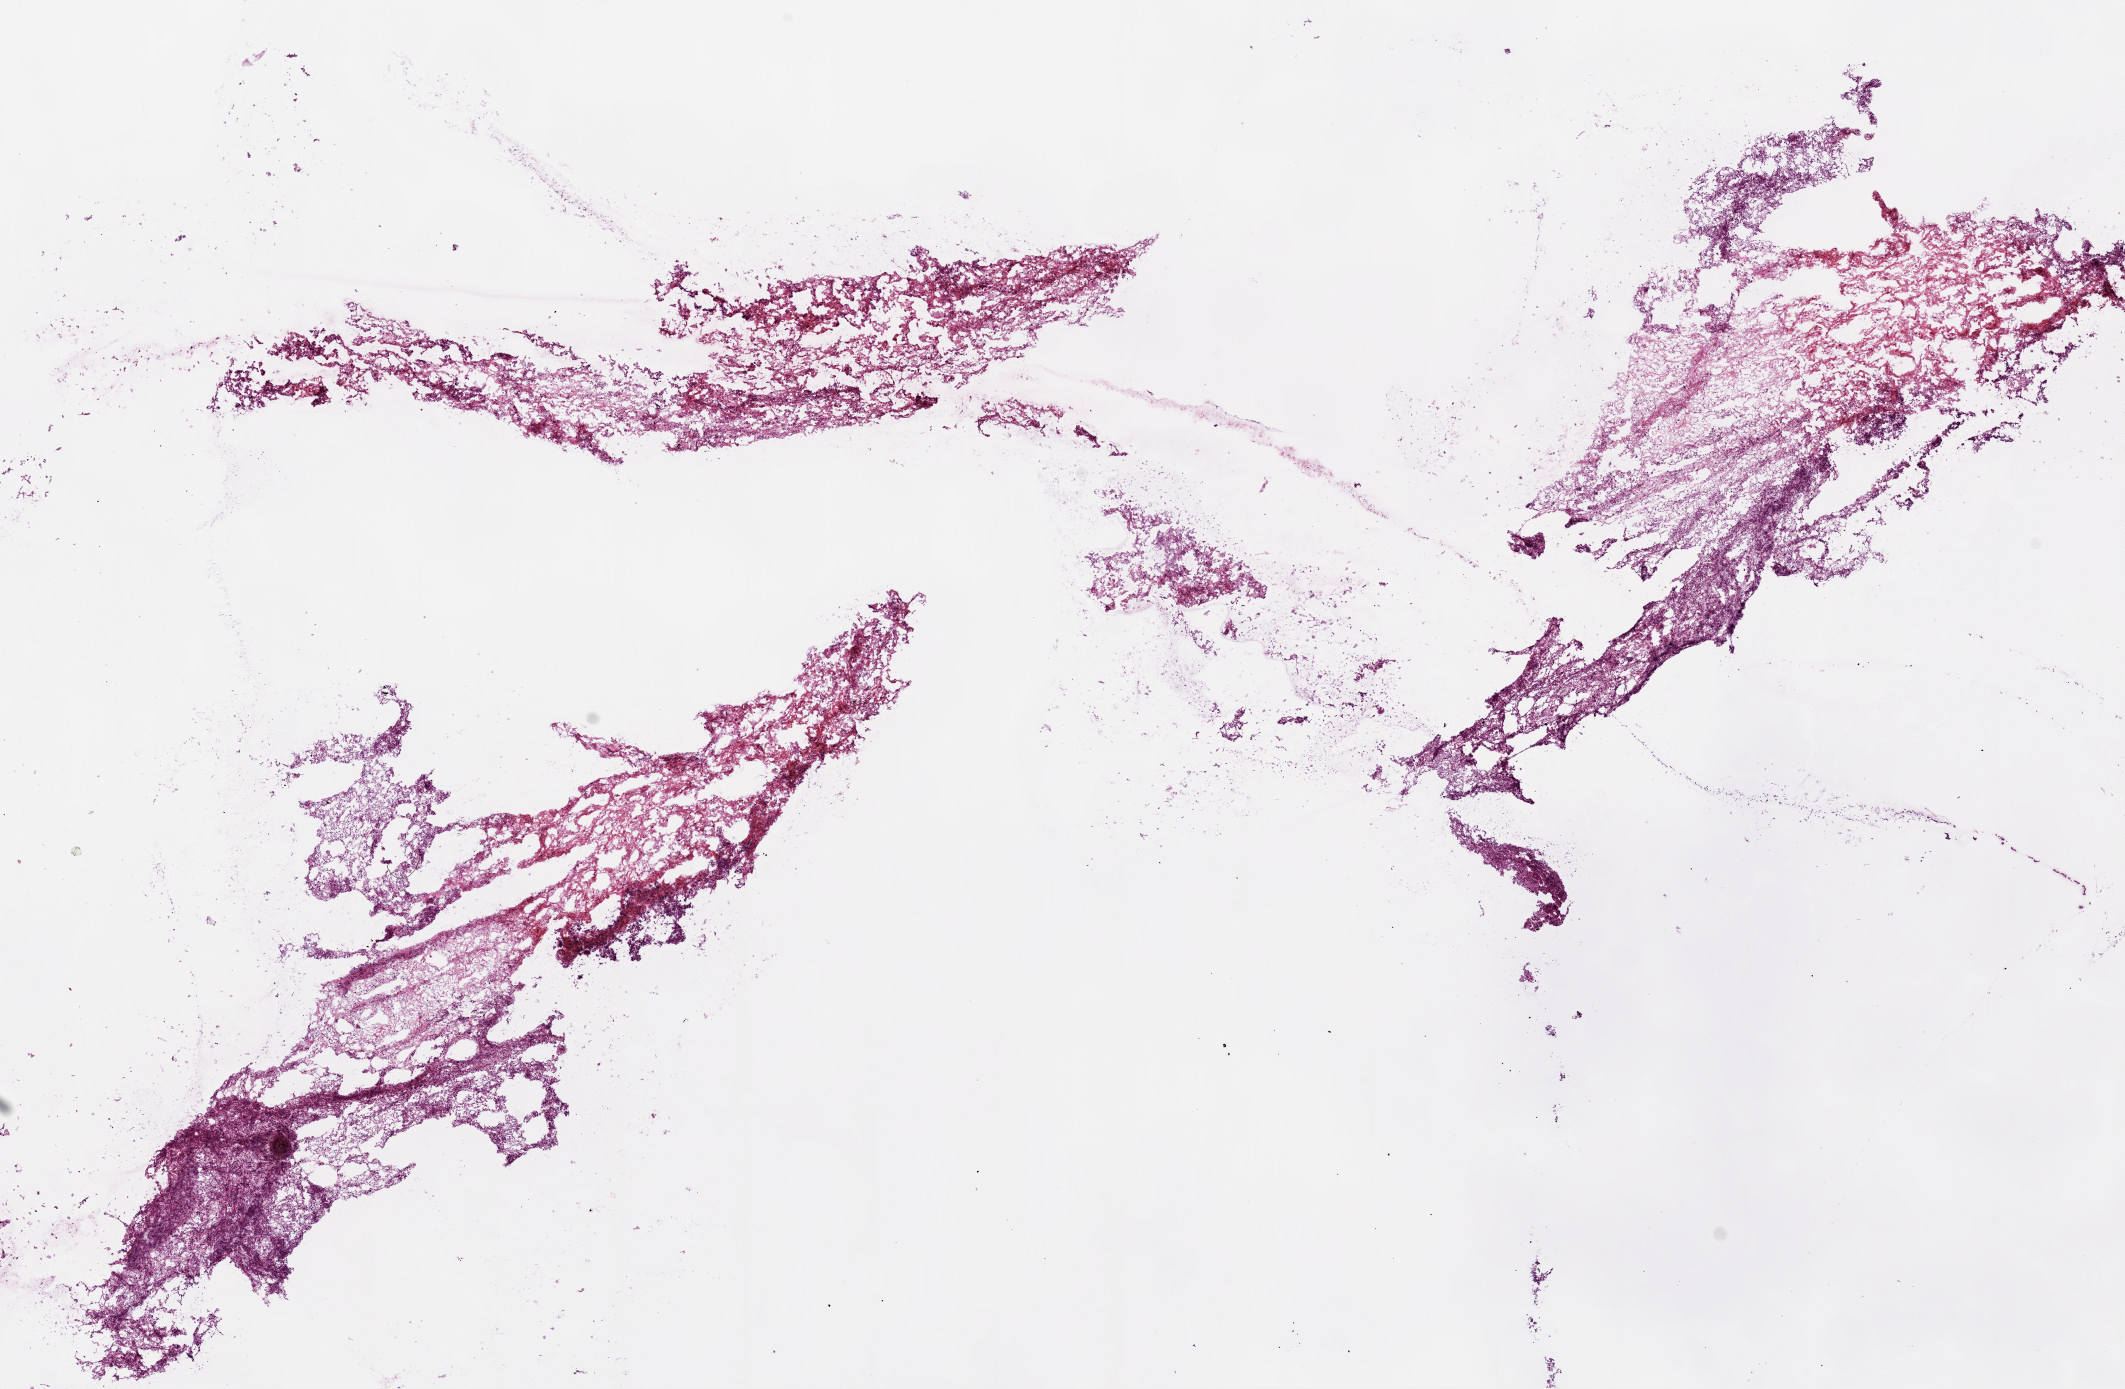
H&E-stained whole-slide image, shown as a low-resolution overview of the whole scanned area (about 17.1 x 11.1 mm, from a 20x scan); frozen section; kidney, primary tumour sample. Male patient; age at initial diagnosis 77 years. Histologic grade: G2 (moderately differentiated). Composition of this section per pathologist review: tumour cells 60%, tumour nuclei 75%, normal cells 0%, stromal cells 40%, necrosis 0%.
Histologic diagnosis: Clear cell adenocarcinoma, NOS. AJCC pathologic stage: I. Laterality: left. TNM: T1a N0 M0.